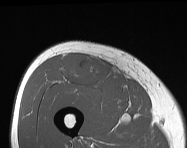
MRI of an extremity soft-tissue mass, one axial slice. MR volume resampled by the dataset authors to the PET/CT grid (not the native acquisition matrix). 187 × 148 image matrix, field of view 183 × 145 mm. Male patient. Case-level facts recorded for this patient, not image findings: histological type: pleiomorphic leiomyosarcoma; grade: intermediate; site of the primary tumour: right thigh.
Annotated regions visible in this slice (expert contour drawn on MRI and transferred to this co-registered scan by the dataset authors):
- gross tumour volume including surrounding oedema: box from (x=63, y=54) to (x=110, y=85) px